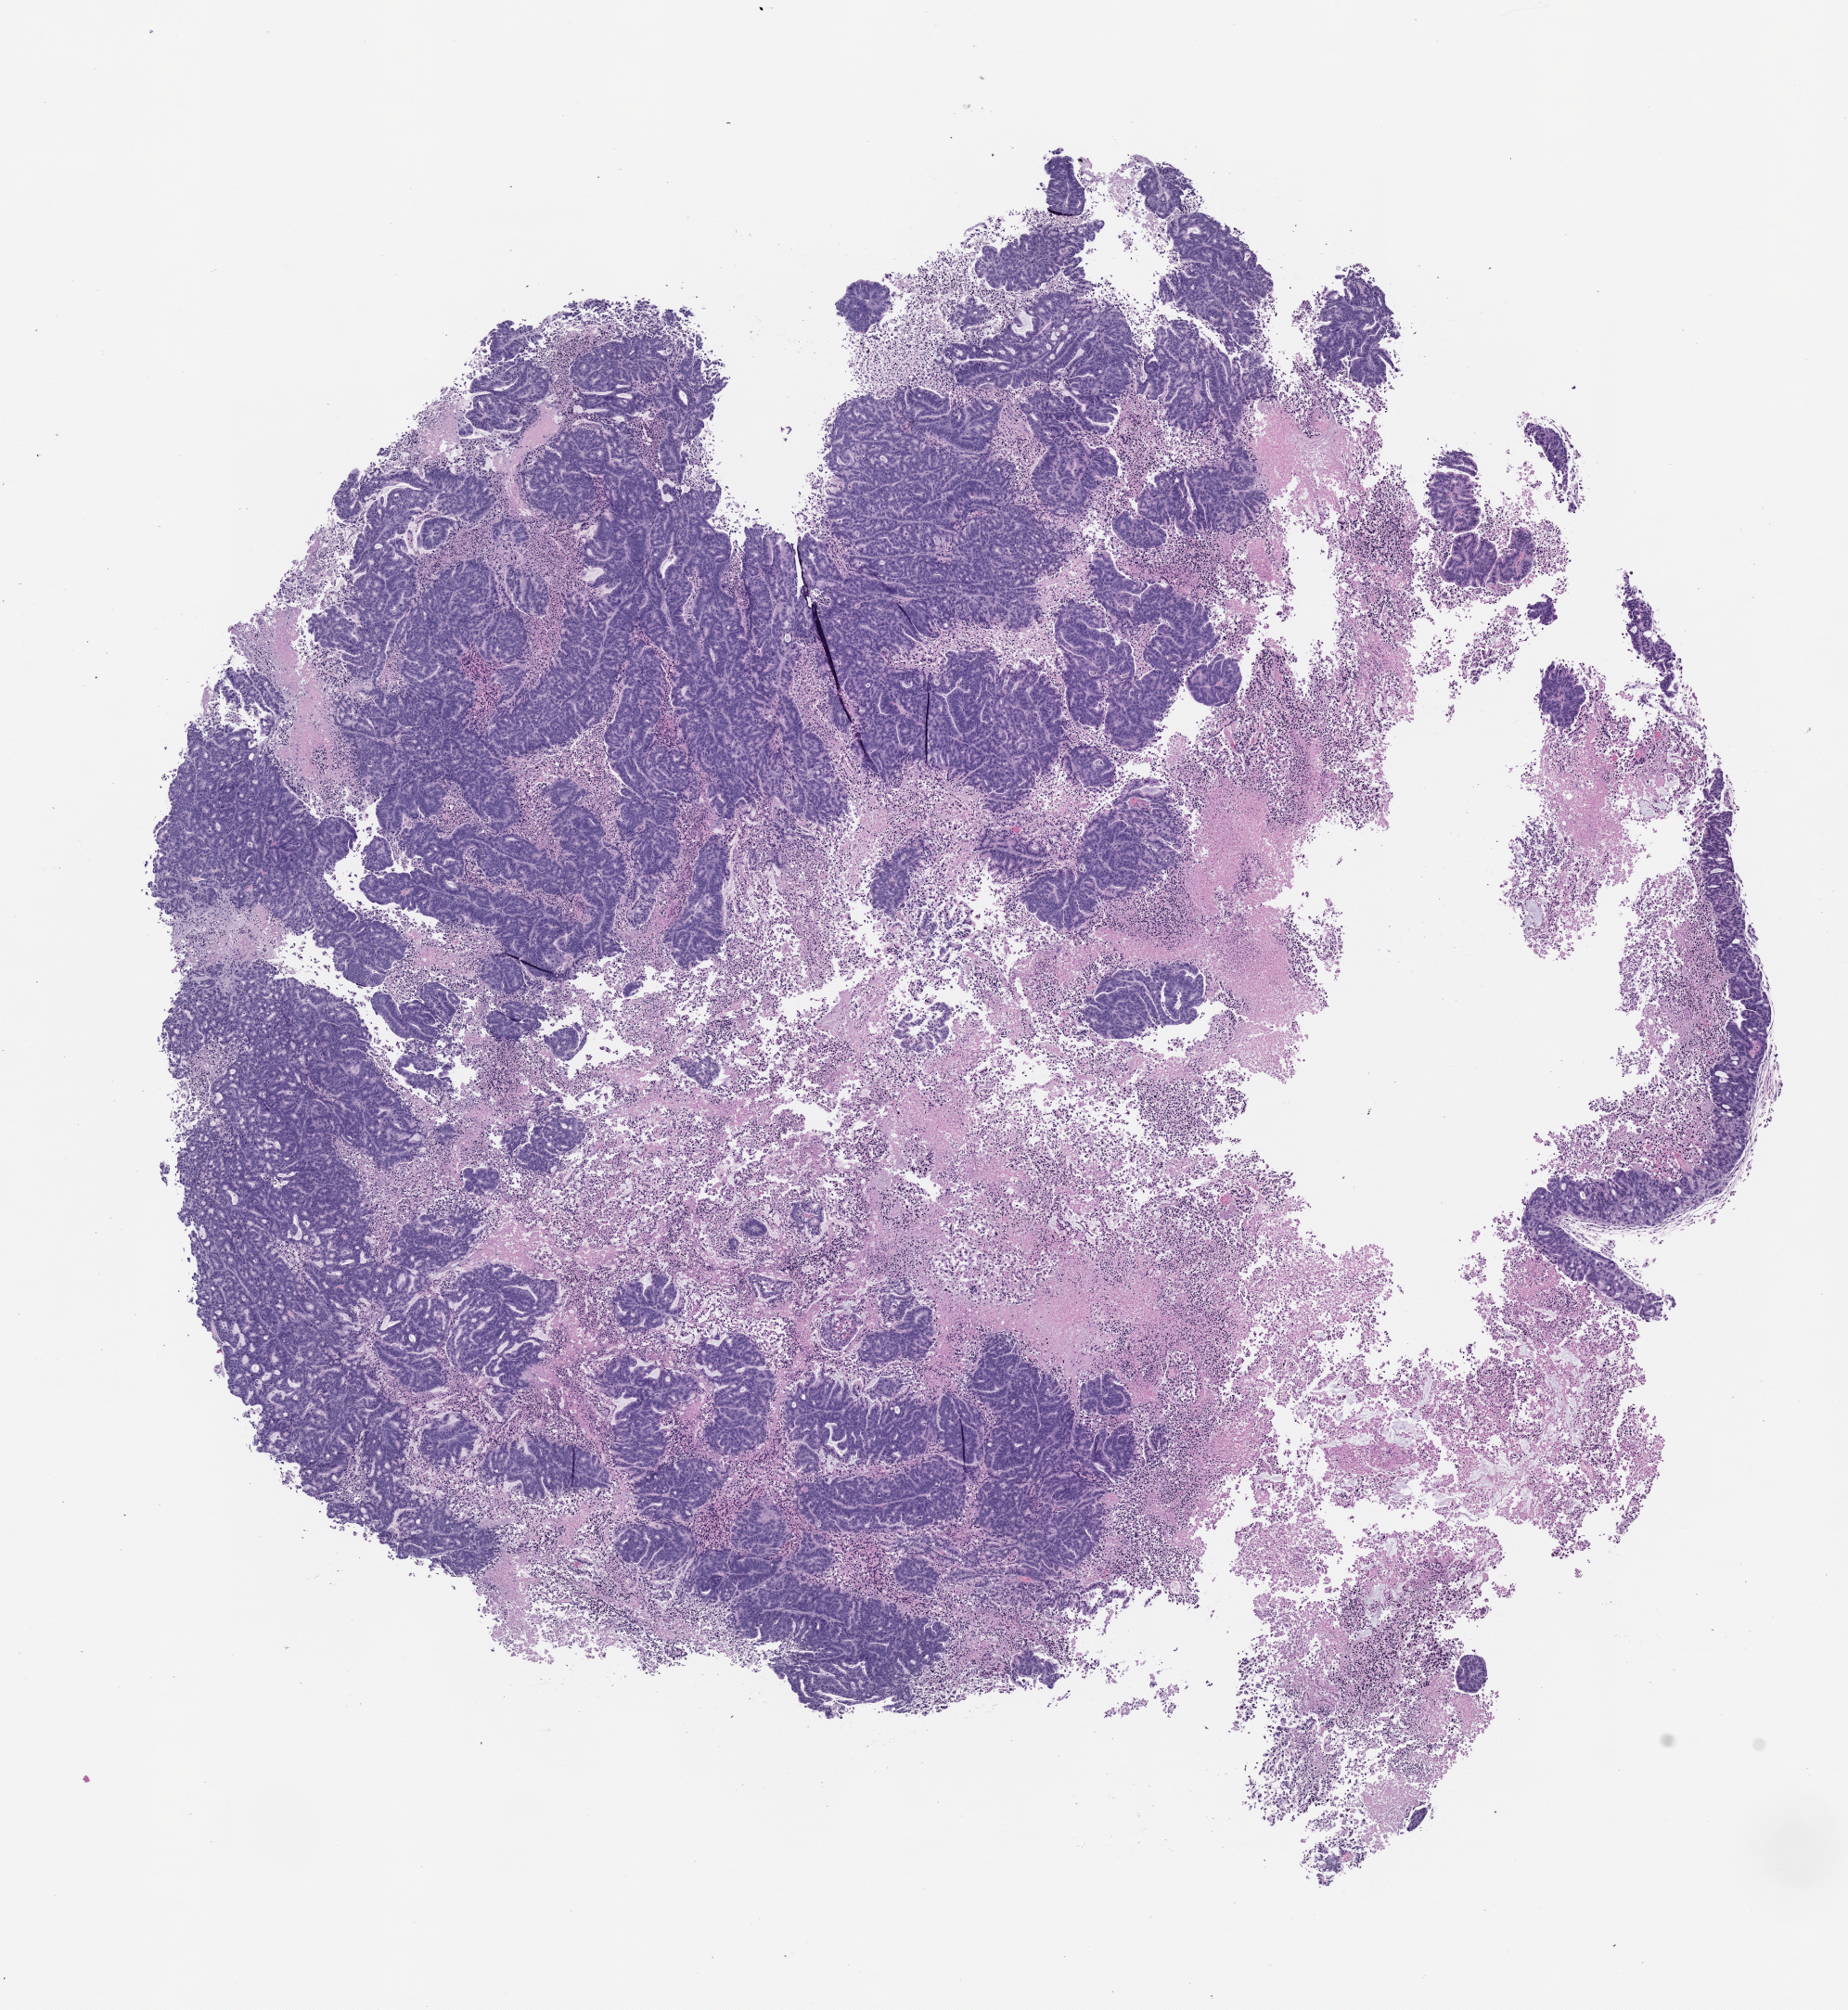
Hematoxylin and eosin (H&E) whole-slide image of a patient-derived xenograft (PDX) tumor grown in a mouse, passage 2, low-resolution overview of the scanned area, about 8.0 x 8.7 mm, formalin-fixed paraffin-embedded section, tumor site category: colon.
Originating patient diagnosis: Colon Adenocarcinoma.